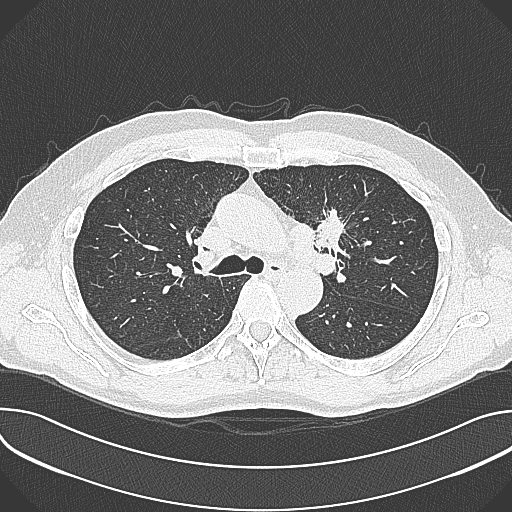
Axial slice from a low-dose chest CT screening exam; first (baseline) screen; lung window (W 1500 / L -600 HU); 1 mm slice thickness; 512 × 512 image matrix. Male, age 59 years at enrolment.
- Lesion marked by an expert reader, box from (x=303, y=195) to (x=364, y=257) px.
- The screening reader recorded 2 non-calcified nodules or masses ≥4 mm on this exam (left upper lobe, left upper lobe); which of them this box marks is not recorded.
- Official screen result: positive, change unspecified: nodule(s) >= 4 mm or enlarging nodule(s), mass(es), or other non-specific abnormalities suspicious for lung cancer.
- Later outcome: lung cancer diagnosed 21 days after this screen — non-small cell carcinoma, left upper lobe, poorly differentiated (G3), stage IIIA (AJCC 6th edition), 35 mm at pathology.